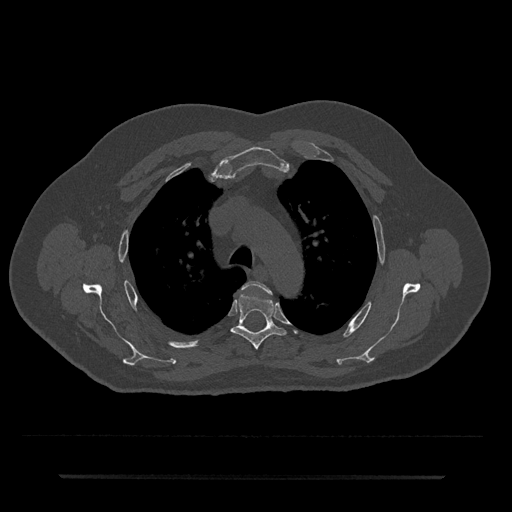
CT including the spine, one axial slice; position 530 of 797 along the scan axis; reconstruction kernel Br40s/3; 120 kVp; bone window (W 1800 / L 400 HU); 0.5 mm slice thickness; 512 × 512 image matrix, field of view 437 × 437 mm. Patient: male, 69 years. From the clinical record (not read from this slice): primary cancer: prostate.
Outlined on this slice (semi-automatically segmented with operator editing):
- T3 vertebra: bounding box (x1, y1, x2, y2) in pixels: (242, 281, 271, 294)
- T4 vertebra: (231, 294, 286, 349)